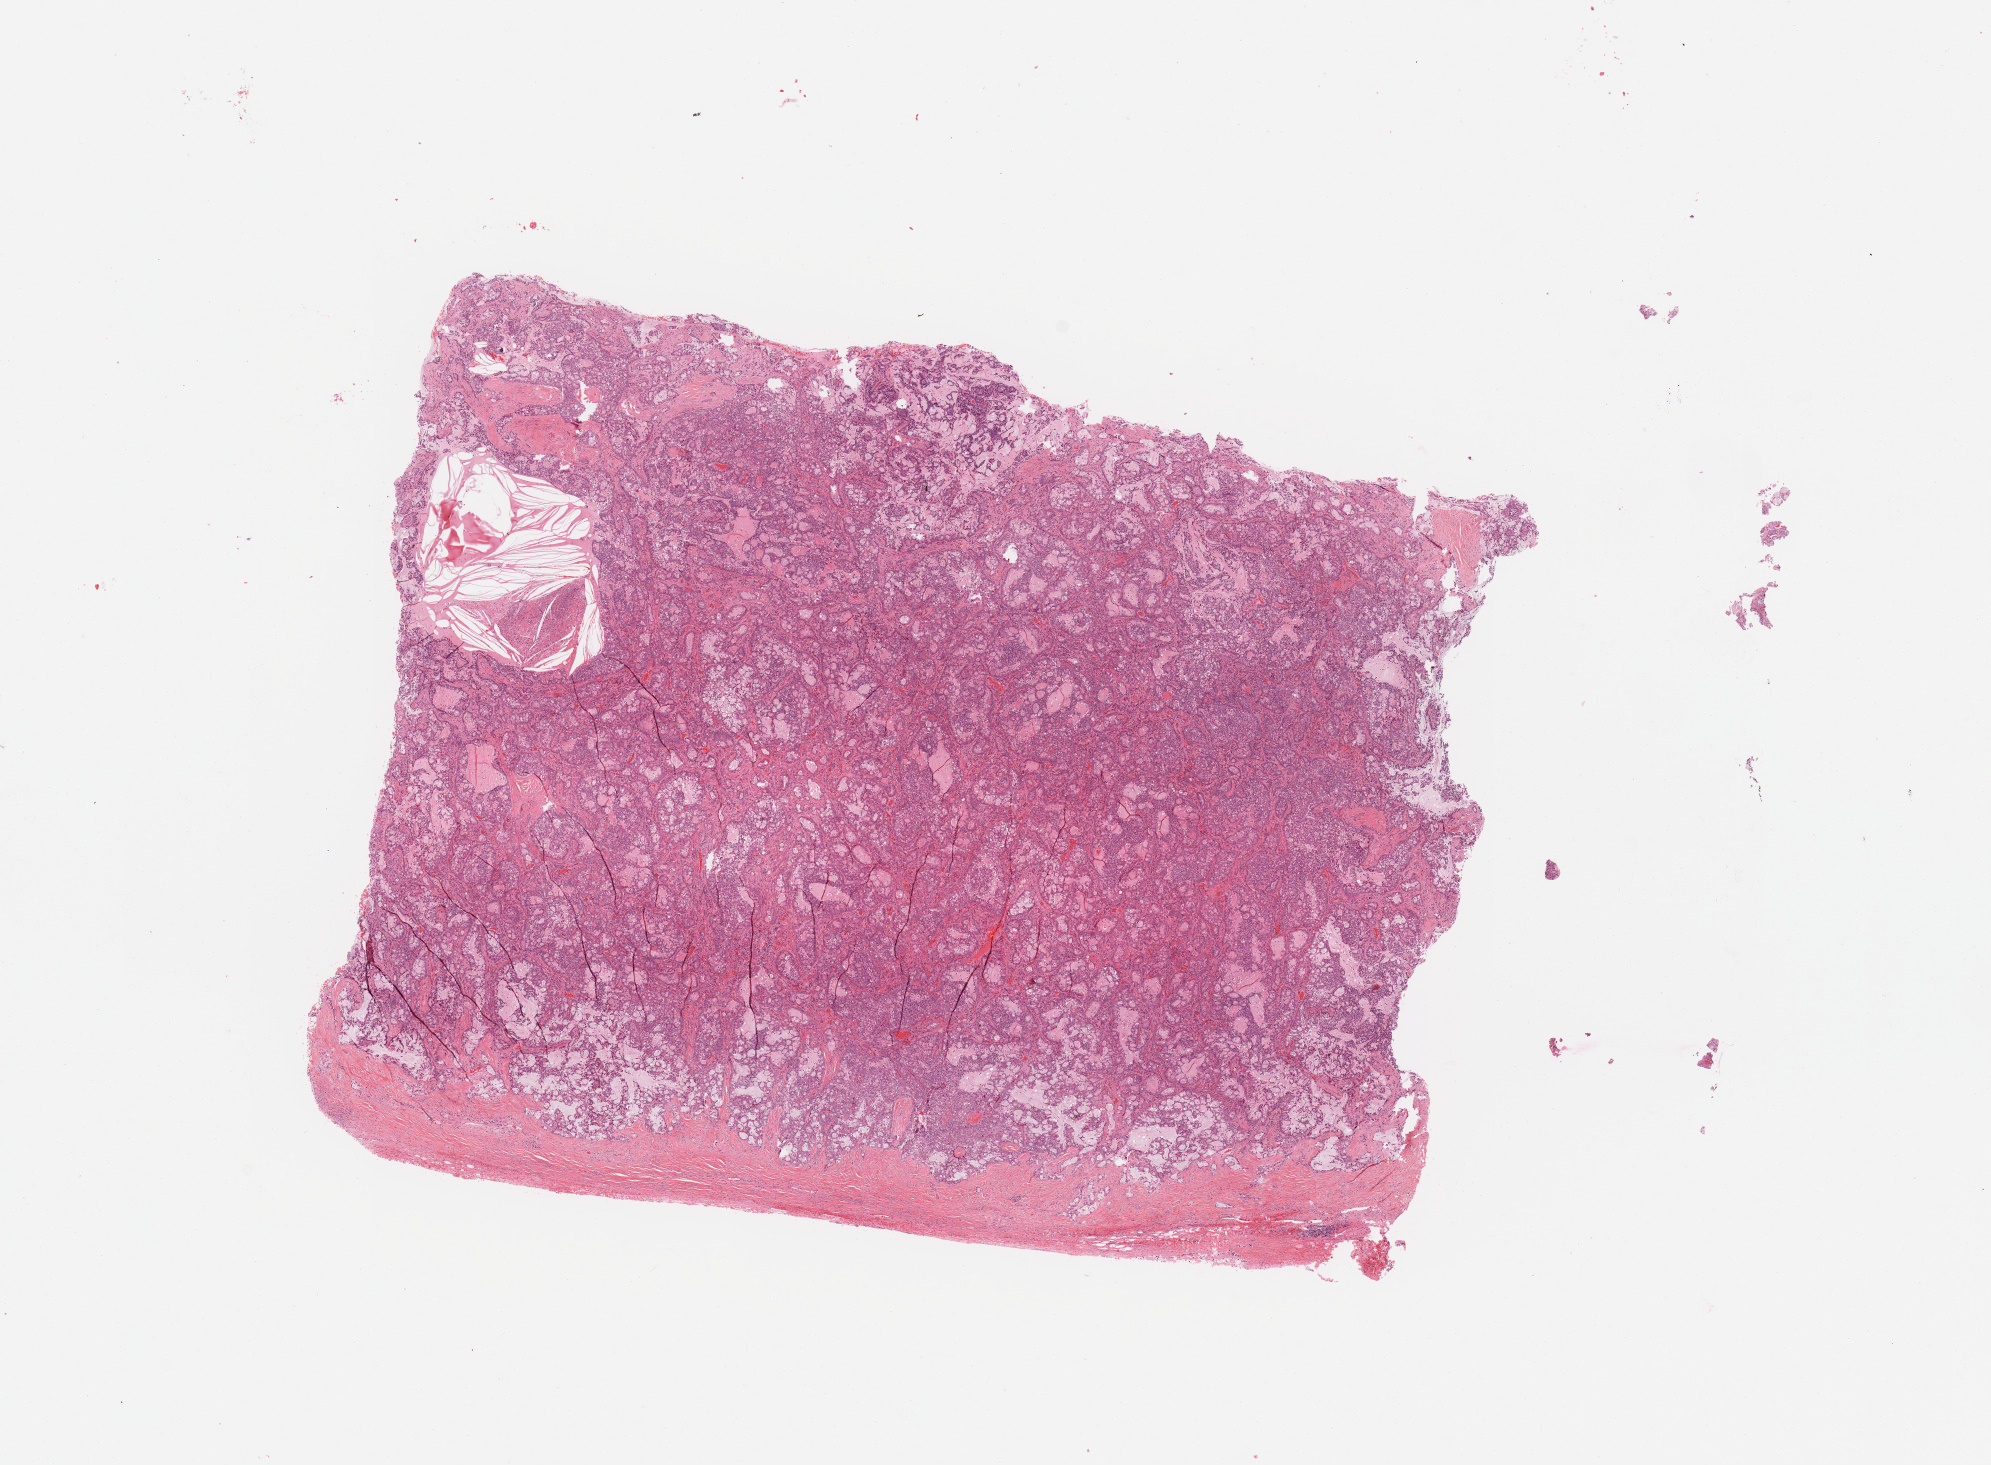
Hematoxylin and eosin (H&E) stained whole-slide image, whole scanned area (about 15.8 x 11.6 mm, slide scanned at 20x) shown as a low-resolution overview, tumour tissue sample, sampled site: lung. Patient: female, age 59 years. Histologic grade: G2 (moderately differentiated). Composition of this section per pathologist review: tumour nuclei 80%, necrosis 0%.
• AJCC pathologic stage: IA
• histologic diagnosis: Adenocarcinoma, NOS
• primary tumour site (as recorded): left lower lobe